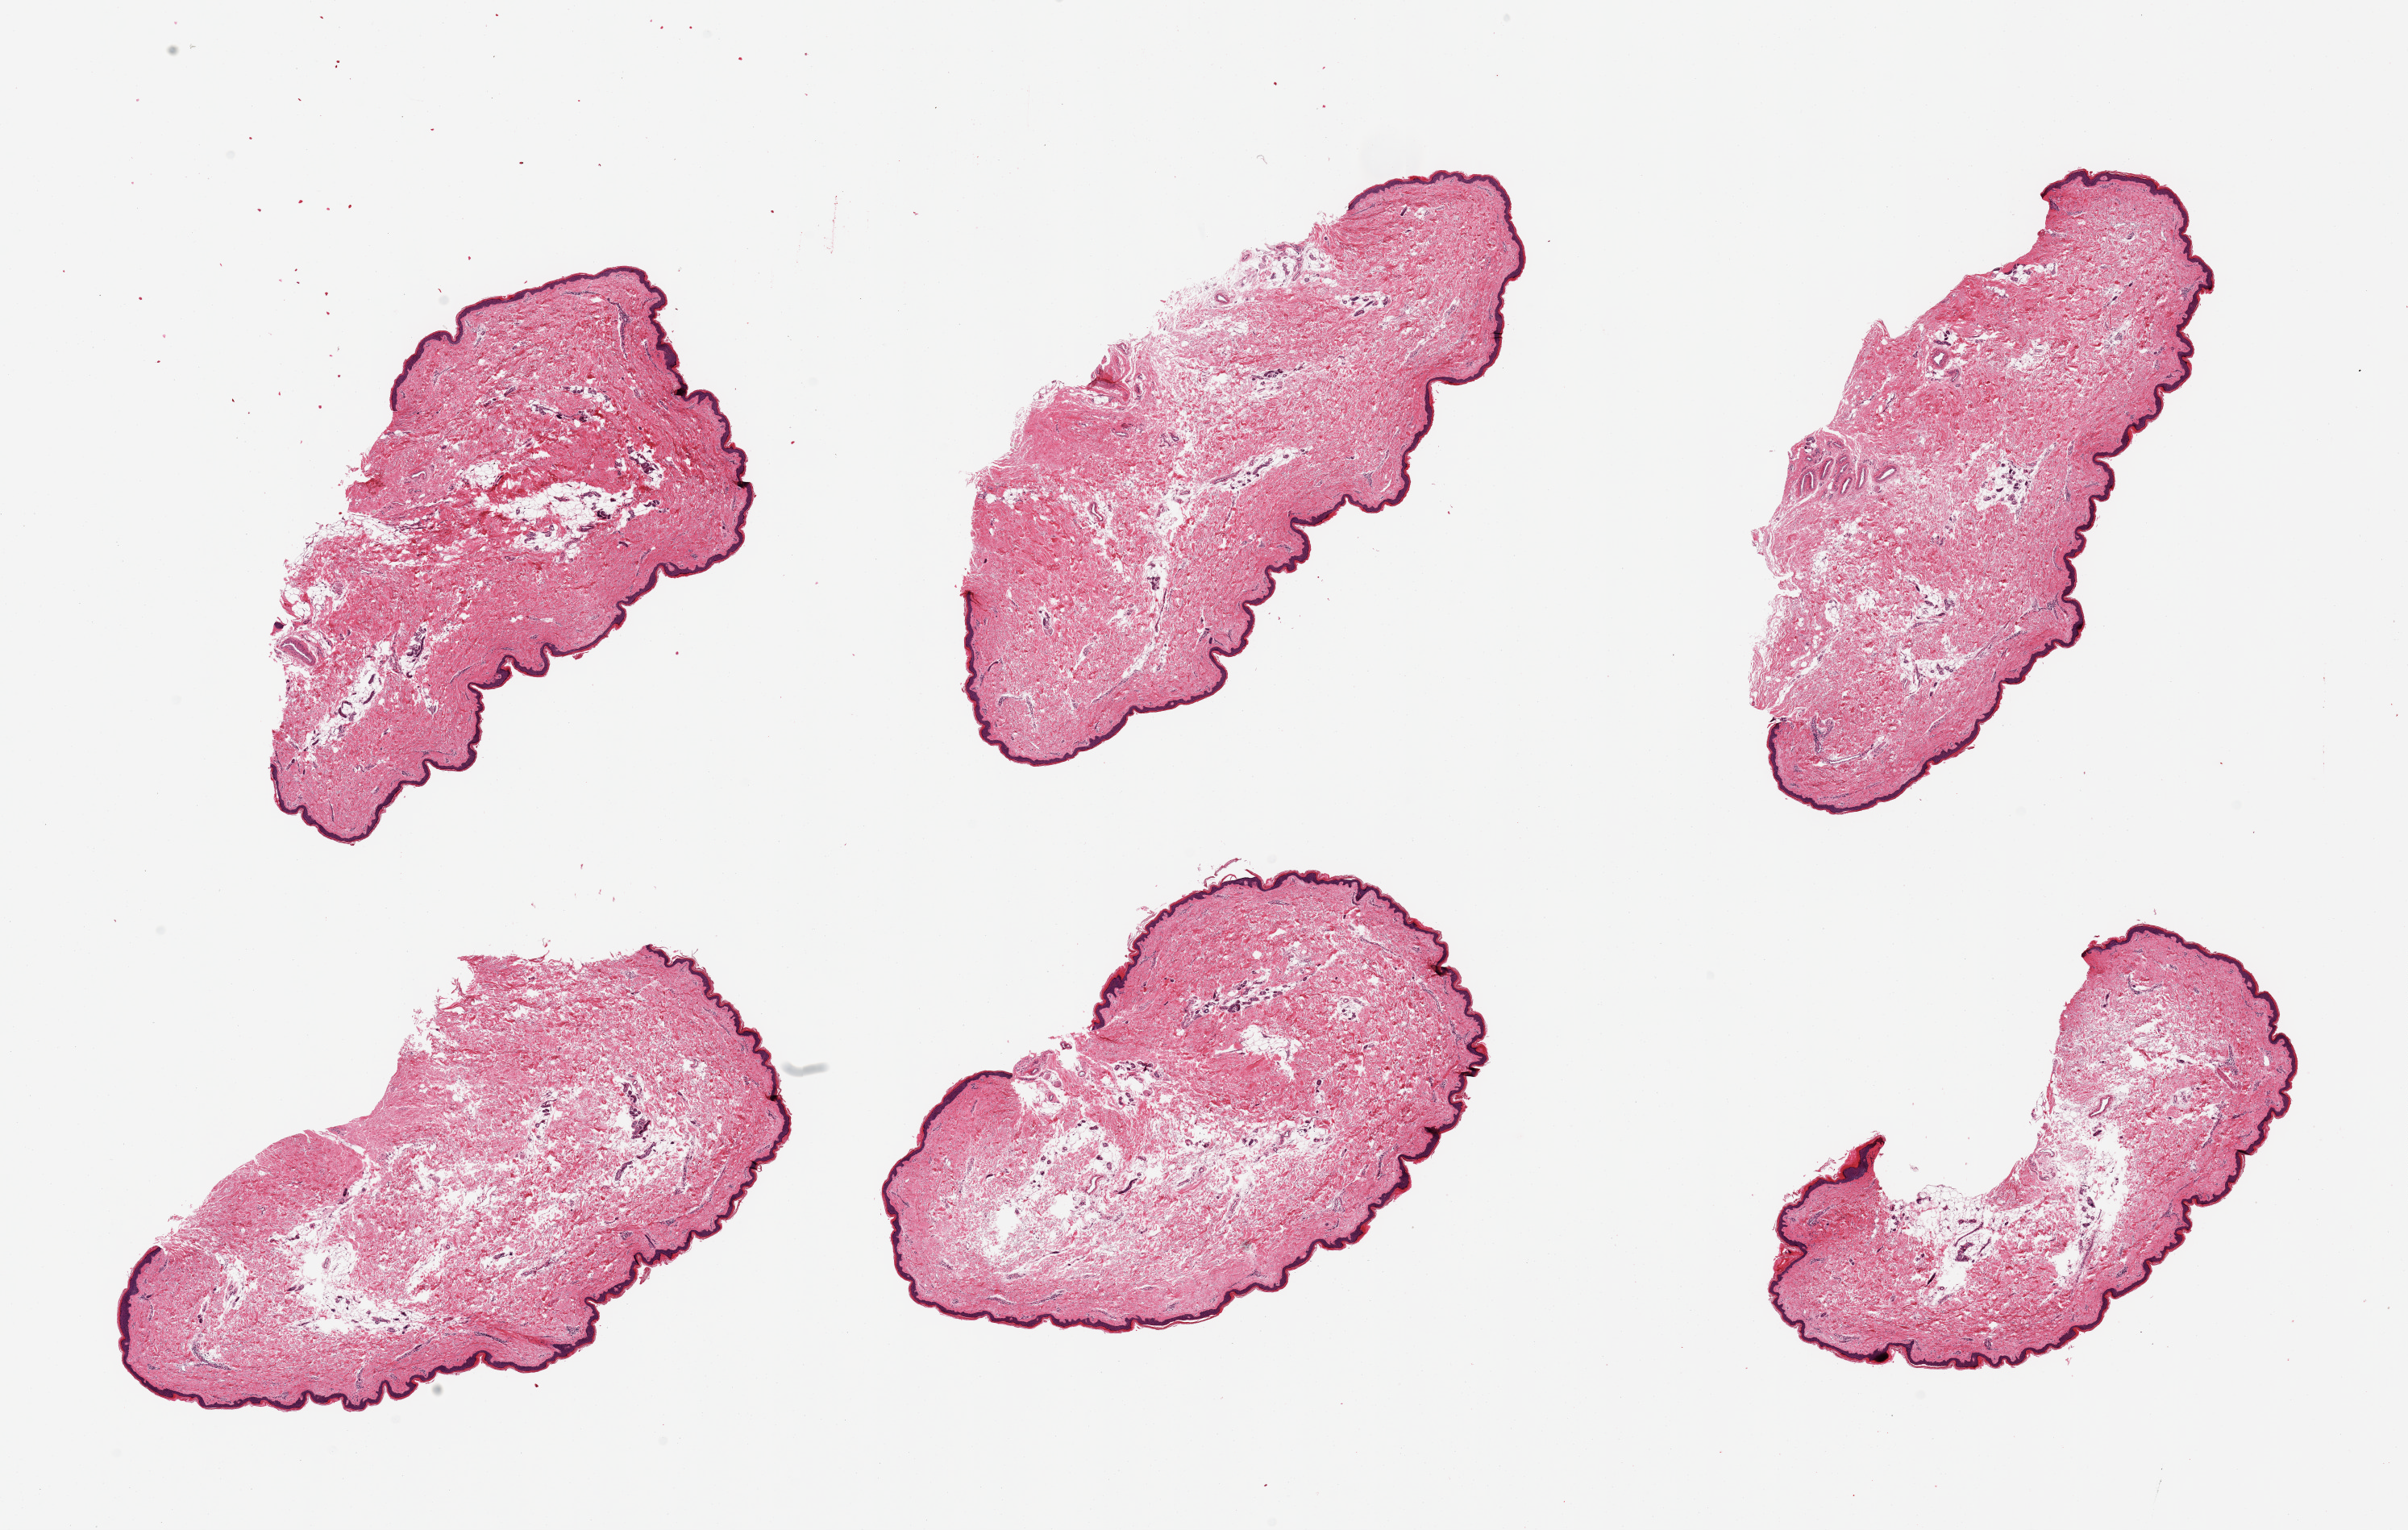
Hematoxylin and eosin (H&E) whole-slide image — low-resolution overview of the scanned area, about 23.6 x 15.0 mm (from a 20x scan), PAXgene-fixed paraffin-embedded (PFPE) section, section of skin of lower leg (target tissue), donor tissue sample.
- review note (as recorded): 6 pieces, no dermal fat, squamous epithelium is ~50 microns